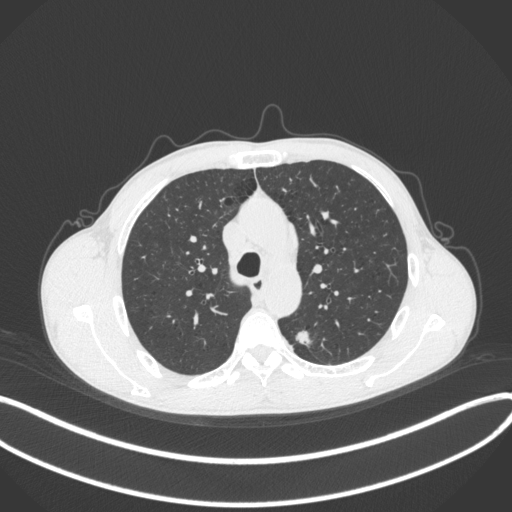
Chest CT, one axial slice; position 280 of 429 along the scan axis; reconstruction kernel B31f; lung window (W 1500 / L -600 HU); 1 mm slice thickness; 512 × 512 image matrix, field of view 400 × 400 mm. Male patient, age 51 years. From the clinical record (not read from this slice): clinical TNM (as recorded): T2a N1 M1.
Outlined on this slice (rectangle marked by the reading radiologist):
- lung tumour (recorded histology: adenocarcinoma): bounding box [x1, y1, x2, y2] px = [293, 327, 318, 349]